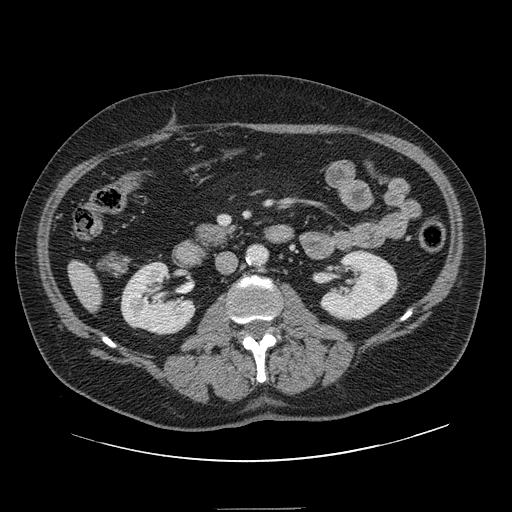
Contrast-enhanced abdominal CT, one axial slice; slice 36 of 154 in the series (ordered by position); intravenous contrast given; soft-tissue window (W 400 / L 40 HU); 2.5 mm slice thickness; 512 × 512 image matrix, field of view 451 × 451 mm. Male patient, age 61 years. Case-level facts recorded for this patient, not image findings: diagnosis: colorectal cancer liver metastases, imaged before liver resection; multiple liver metastases: yes; largest metastasis: 2.6 cm; chemotherapy before resection: no.
Outlined on this slice (outlined manually by an expert reader):
- liver: bounding box (x1, y1, x2, y2) in pixels: (70, 263, 103, 310)
- planned liver remnant (the part of the liver to remain after resection): (70, 263, 103, 310)